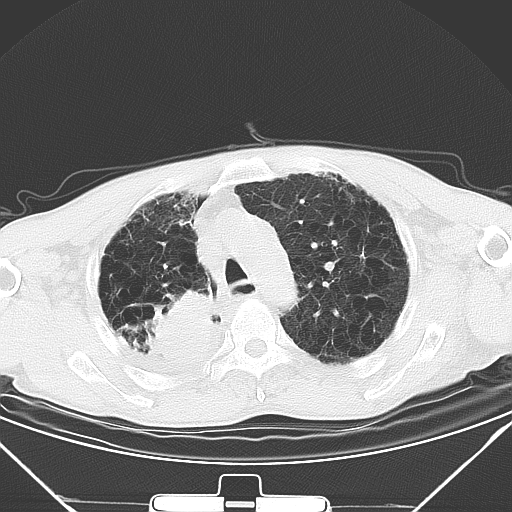
Chest CT, one axial slice. Slice 37 of 50 in the series (ordered by position). 120 kVp. Lung window (W 1500 / L -600 HU). 5 mm slice thickness. 512 × 512 image matrix, field of view 373 × 373 mm. Patient: male, 65 years. From the clinical record (not read from this slice): clinical TNM (as recorded): T3 N1 M1a.
Annotated regions visible in this slice (bounding box drawn by a radiologist):
- lung tumour (recorded histology: squamous cell carcinoma): box from (x=142, y=286) to (x=208, y=363) px